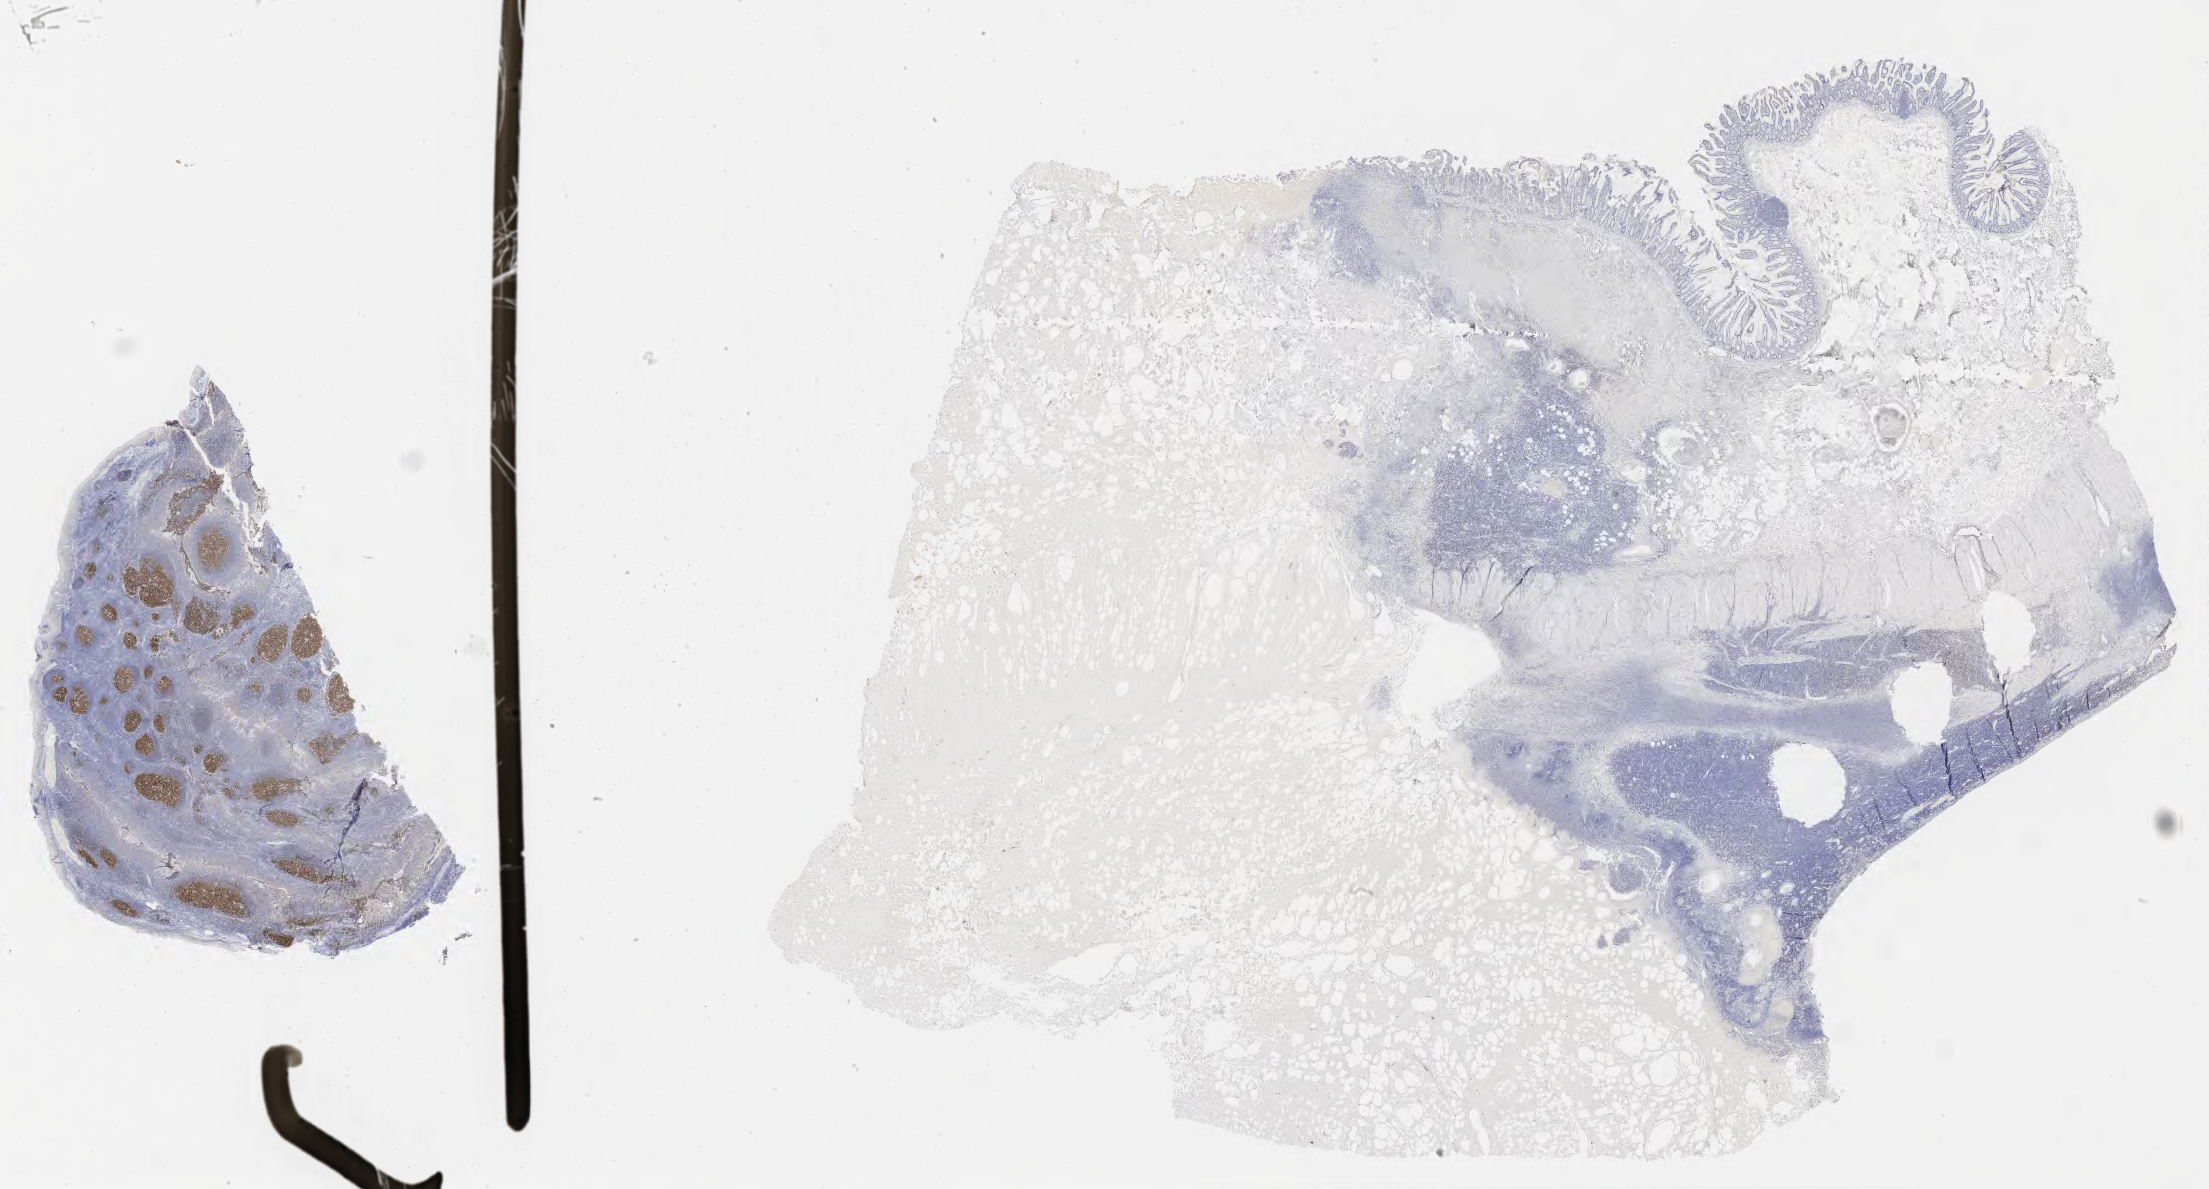
IHC for BCL6, whole-slide image, low-resolution overview of the scanned area, about 35.7 x 19.2 mm, specimen: tumor tissue, anatomic site: colon. Patient: male, 62 years old.
* diagnosis: Burkitt lymphoma, NOS